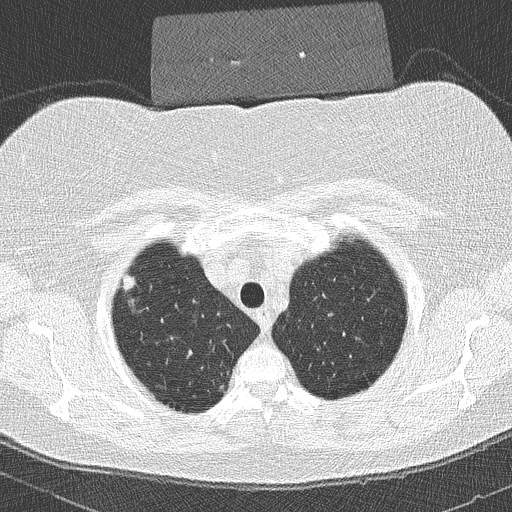
Low-dose screening chest CT, axial slice. Second annual screen. Lung window (W 1500 / L -600 HU). 2 mm slice thickness. 512 × 512 image matrix. Female, age 58 years at enrolment.
• Lesion marked by an expert reader, bounding box (x1, y1, x2, y2) in pixels: (111, 269, 148, 310).
• The screening reader recorded 2 non-calcified nodules or masses ≥4 mm on this exam; which of them this box marks is not recorded.
• Later outcome: lung cancer diagnosed 447 days after this screen (after the third annual screen) — bronchiolo-alveolar adenocarcinoma, NOS, right upper lobe, well differentiated (G1), stage IA (AJCC 6th edition), 9 mm at pathology.